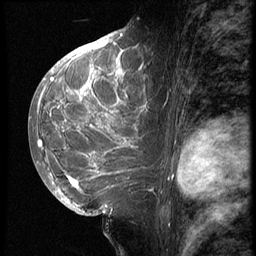
Breast MRI (dynamic contrast-enhanced), one sagittal slice. Slice 33 of 62 in the series (ordered by position). 3 images stored at this slice position (order not interpretable as contrast timing). 1.5 T. TE 4.2 ms, TR 9 ms. 256 × 256 image matrix, field of view 180 × 180 mm. Patient: female, 28 years. Case-level facts recorded for this patient, not image findings: setting: breast cancer imaged before/during neoadjuvant chemotherapy.
Annotated regions visible in this slice (semi-automatic segmentation, software-assisted and operator-edited):
- analysis volume of interest (the breast-tissue region the enhancement analysis was run in; not a lesion): box from (x=42, y=45) to (x=161, y=207) px
- tumour enhancement mask (voxels above the 140 % enhancement threshold inside the analysis volume of interest): (x=45, y=45)–(x=154, y=192)